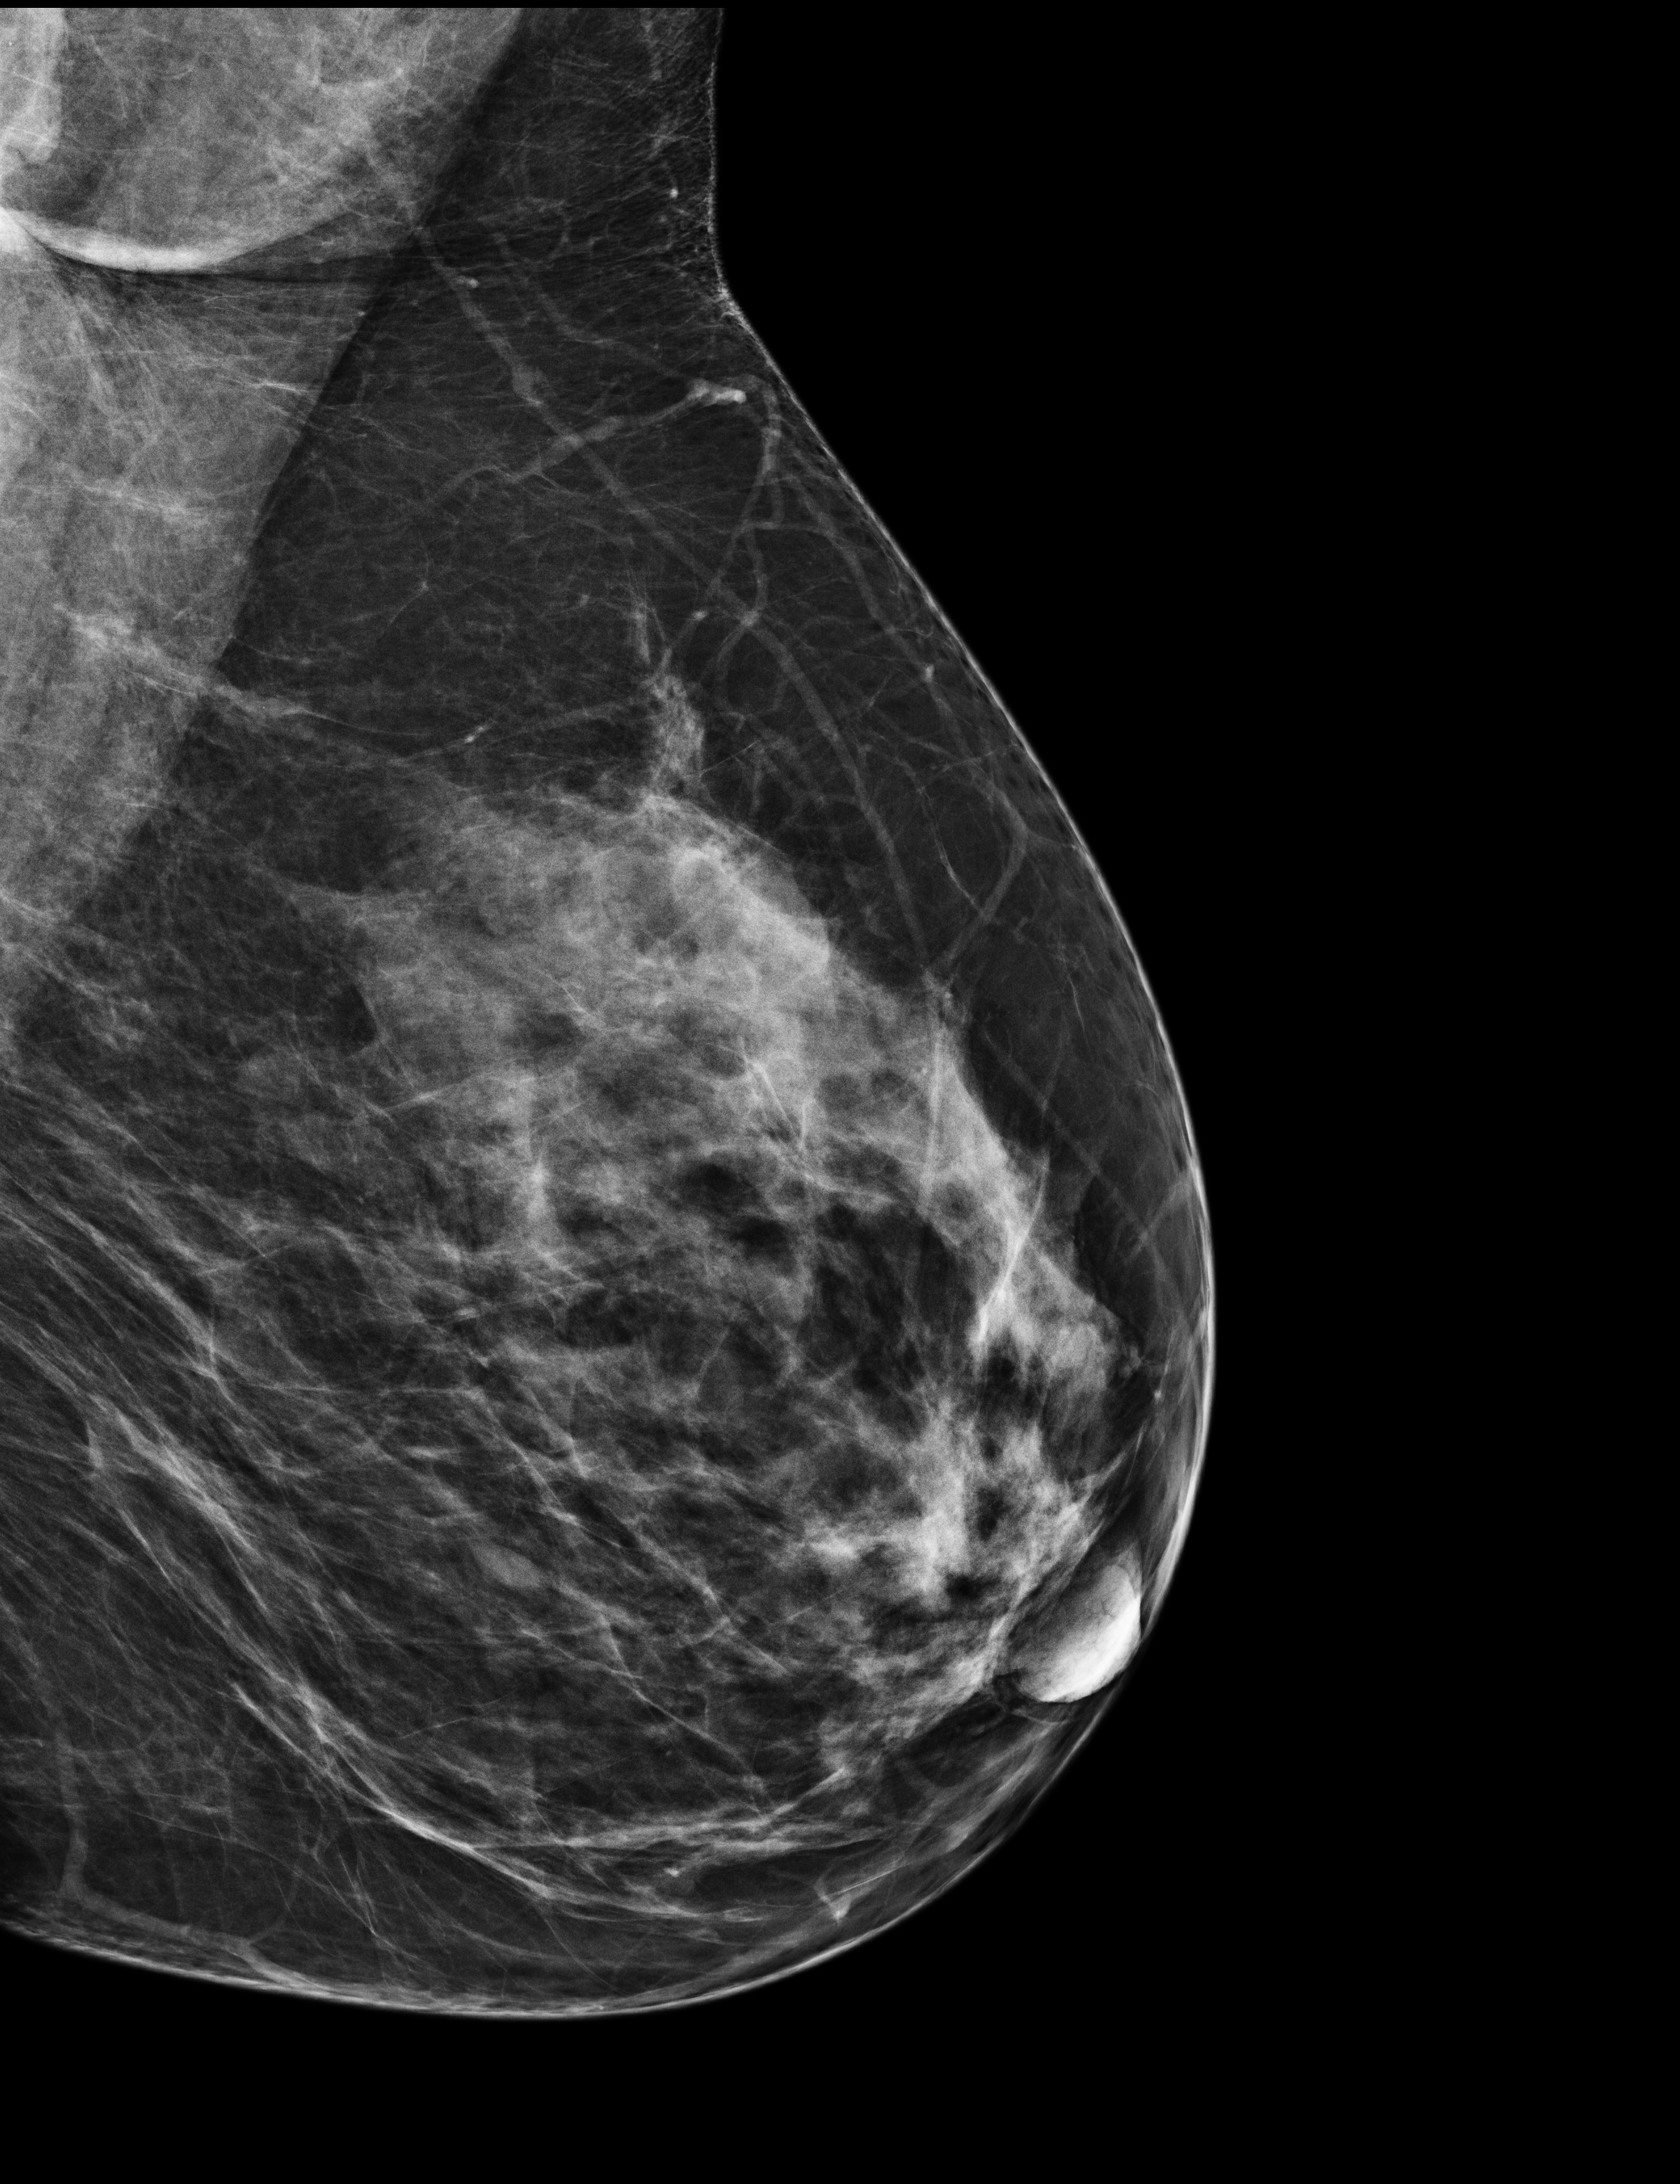
Screening examination. Female patient, age 42 years.
Image type: full-field digital mammogram. Breast: left. Projection: medio-lateral oblique projection.